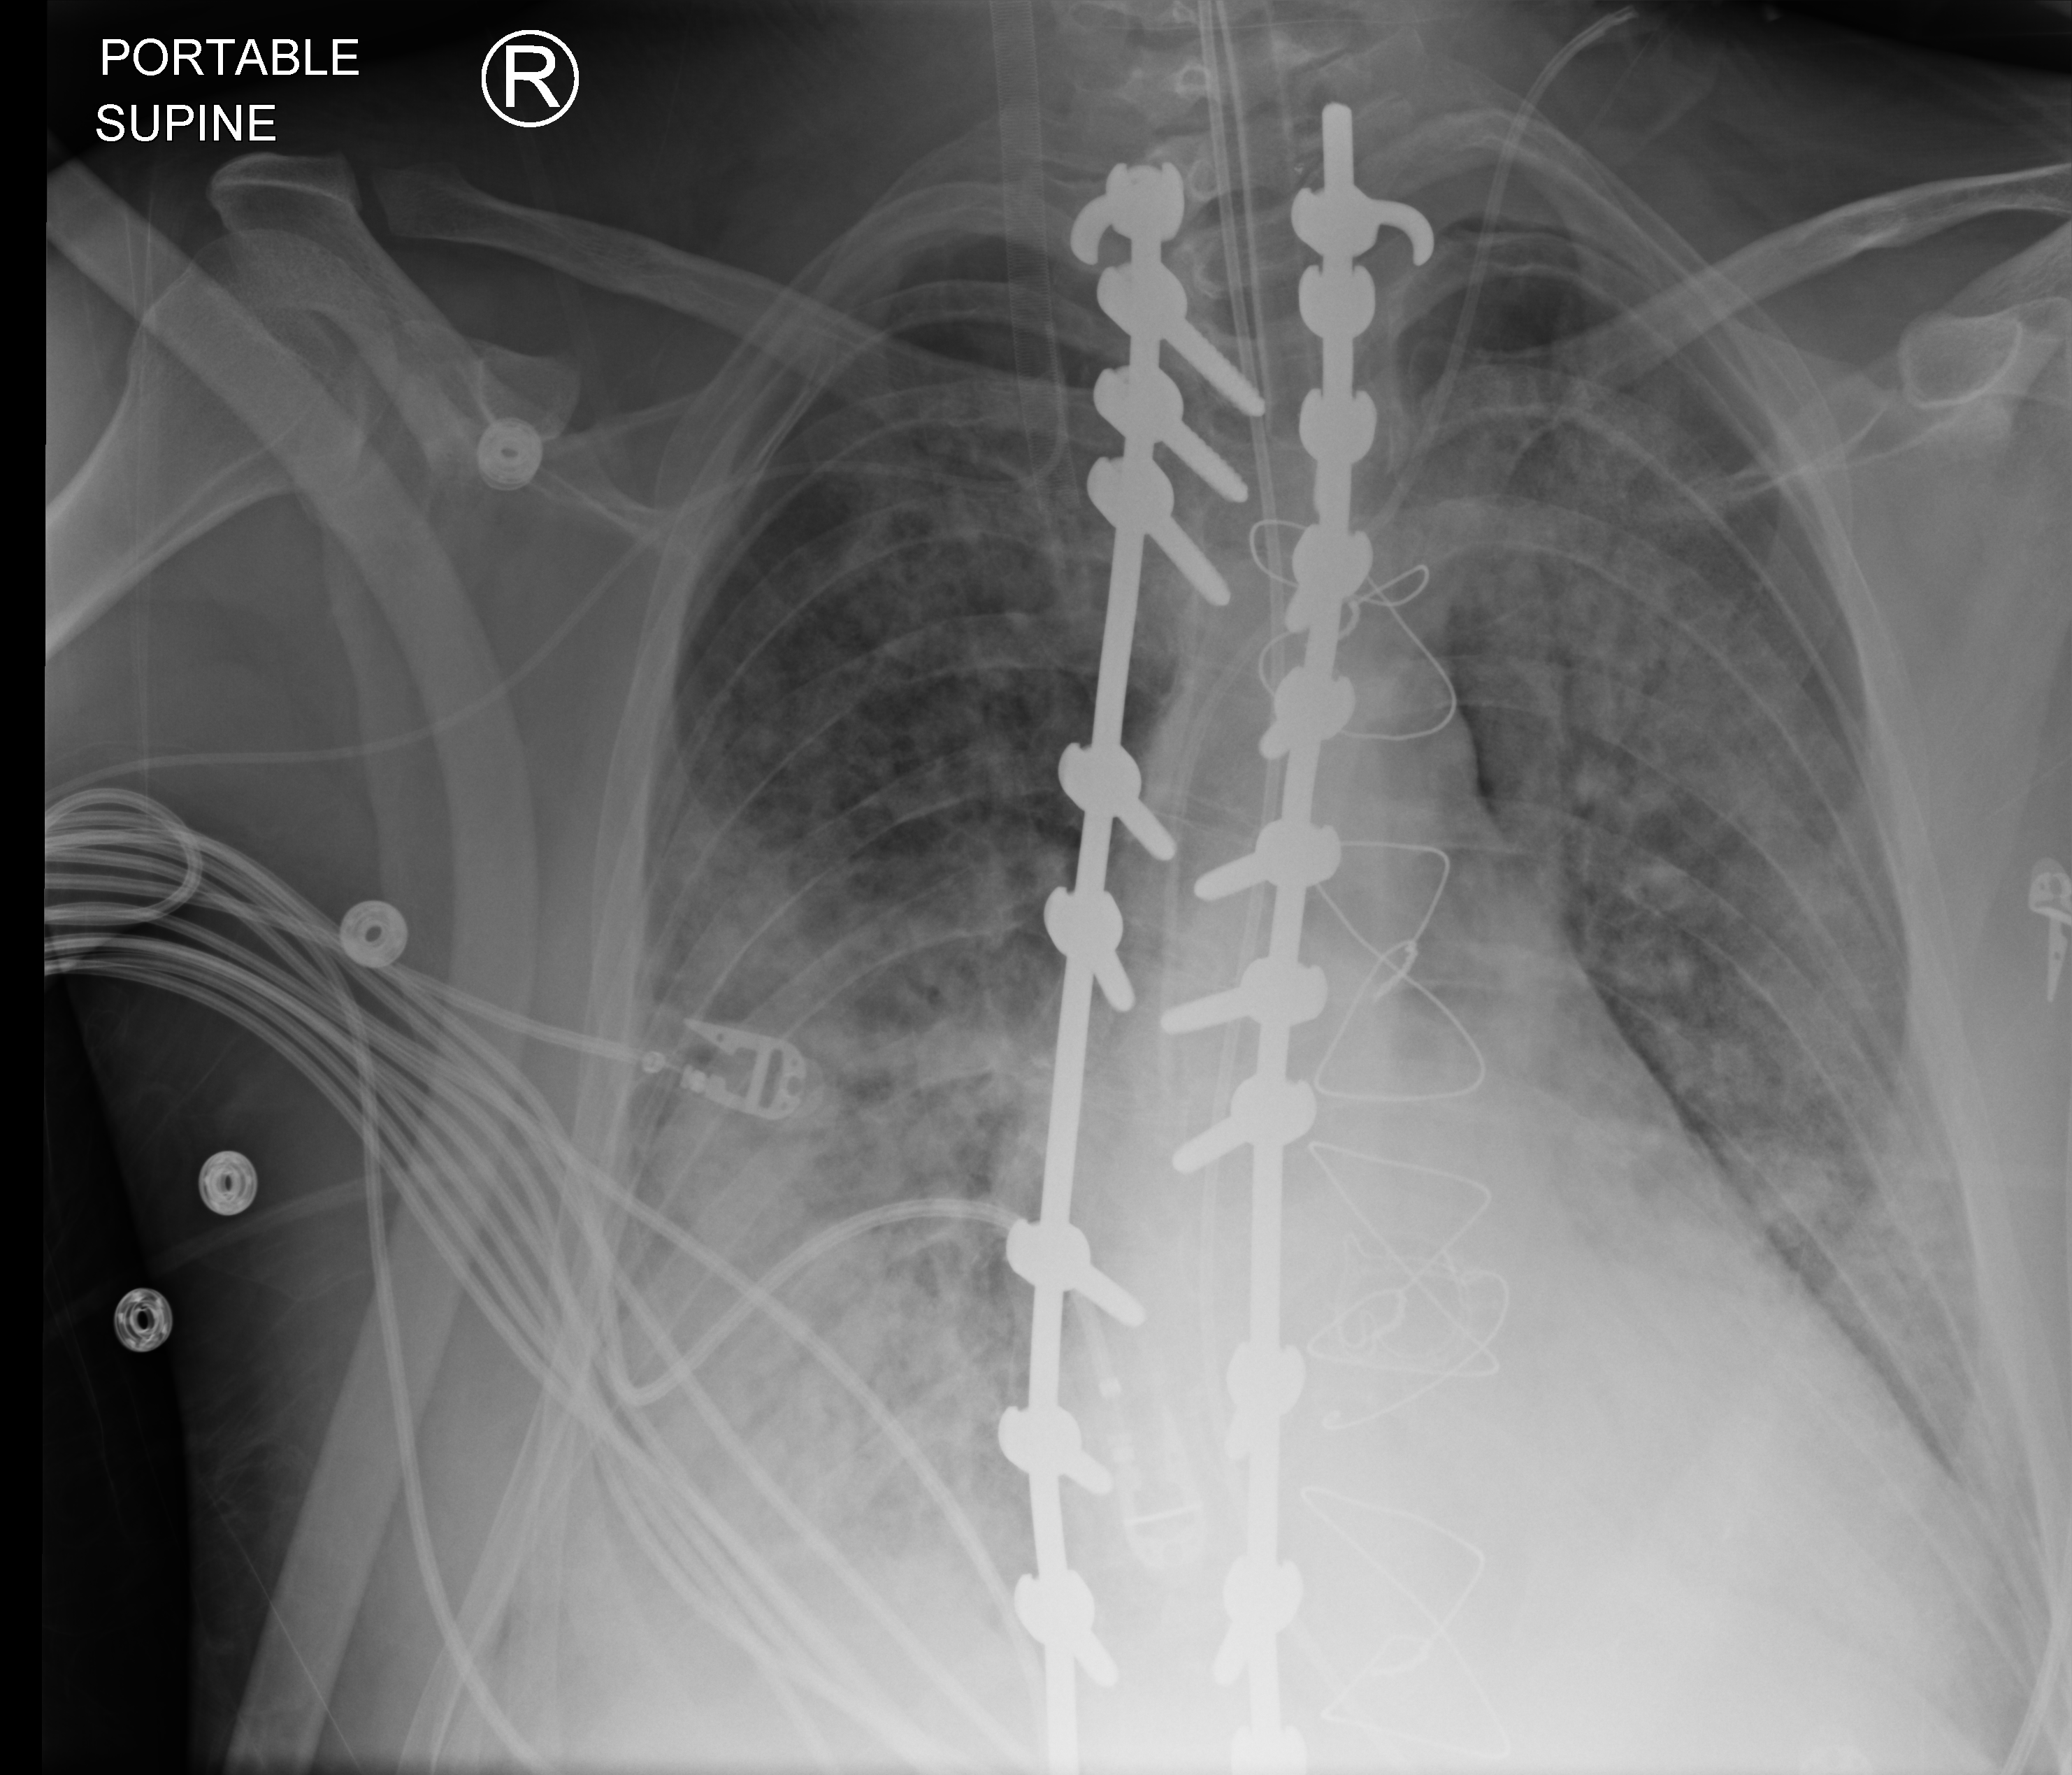
Chest X-ray (portable); anteroposterior (AP) projection. Adult patient hospitalised with COVID-19, age 18–59 years.
Admission-level facts for this patient (not findings on this image; timing relative to this image not recorded): admitted to intensive care during this hospital stay: yes; mechanically ventilated during this hospital stay: yes; chronic kidney disease (admission record): no.